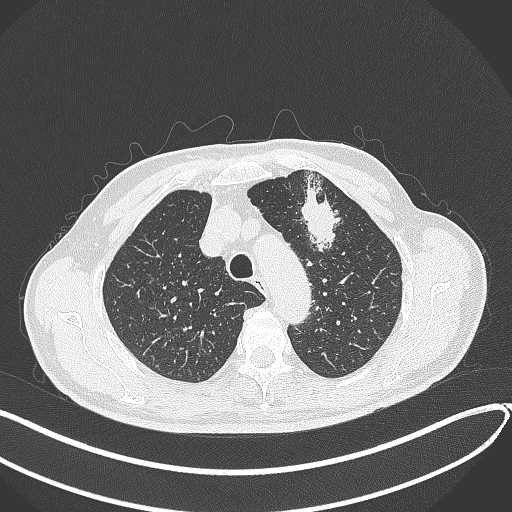
Chest CT, one axial slice; slice 330 of 459 in the series (ordered by position); 120 kVp; lung window (W 1500 / L -600 HU); 1 mm slice thickness; 512 × 512 image matrix. Patient: male, 74 years. From the clinical record (not read from this slice): clinical TNM (as recorded): T2b N0 M1c.
Structures marked on this image (rectangle marked by the reading radiologist):
- lung tumour (recorded histology: adenocarcinoma): box from (x=300, y=179) to (x=345, y=253) px